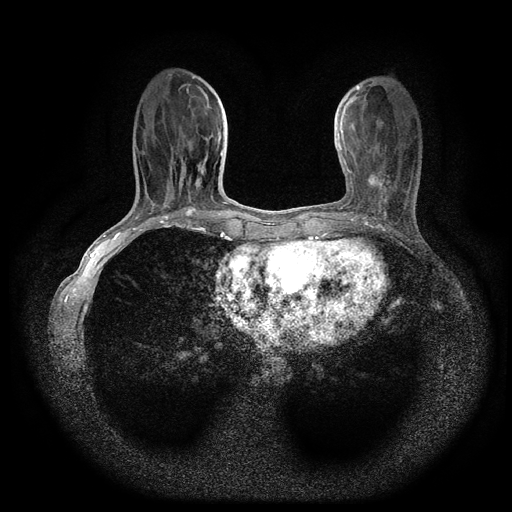
Breast MRI (dynamic contrast-enhanced, multi-phase), one axial slice; dynamic contrast-enhanced series, time point 2 of 5 at this slice position (early post-contrast); 1.5 T; TE 2.7 ms, TR 5.4 ms; 2 mm slice thickness; 512 × 512 image matrix, field of view 330 × 330 mm. Patient: female, 49 years.
Outlined on this slice (semi-automatically segmented with operator editing):
- breast lesion (labelled 'tumour' in the annotation; benign lesions carry a separate 'benign' label): bounding box [x1, y1, x2, y2] px = [367, 171, 387, 192]